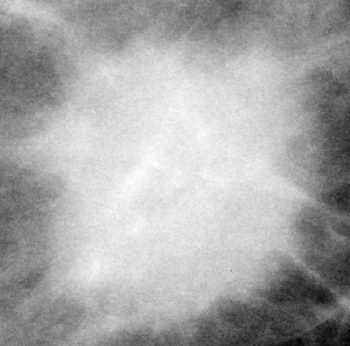
Region of interest cut from a scanned film mammogram (one marked finding); left breast; CC view; BI-RADS breast density category 2 (scale 1–4).
Marked abnormality: mass, shape round, margins spiculated; BI-RADS assessment category 4; subtlety rating 5 on a 1 (subtle) to 5 (obvious) scale; pathology result (as recorded, not read from the image): malignant.